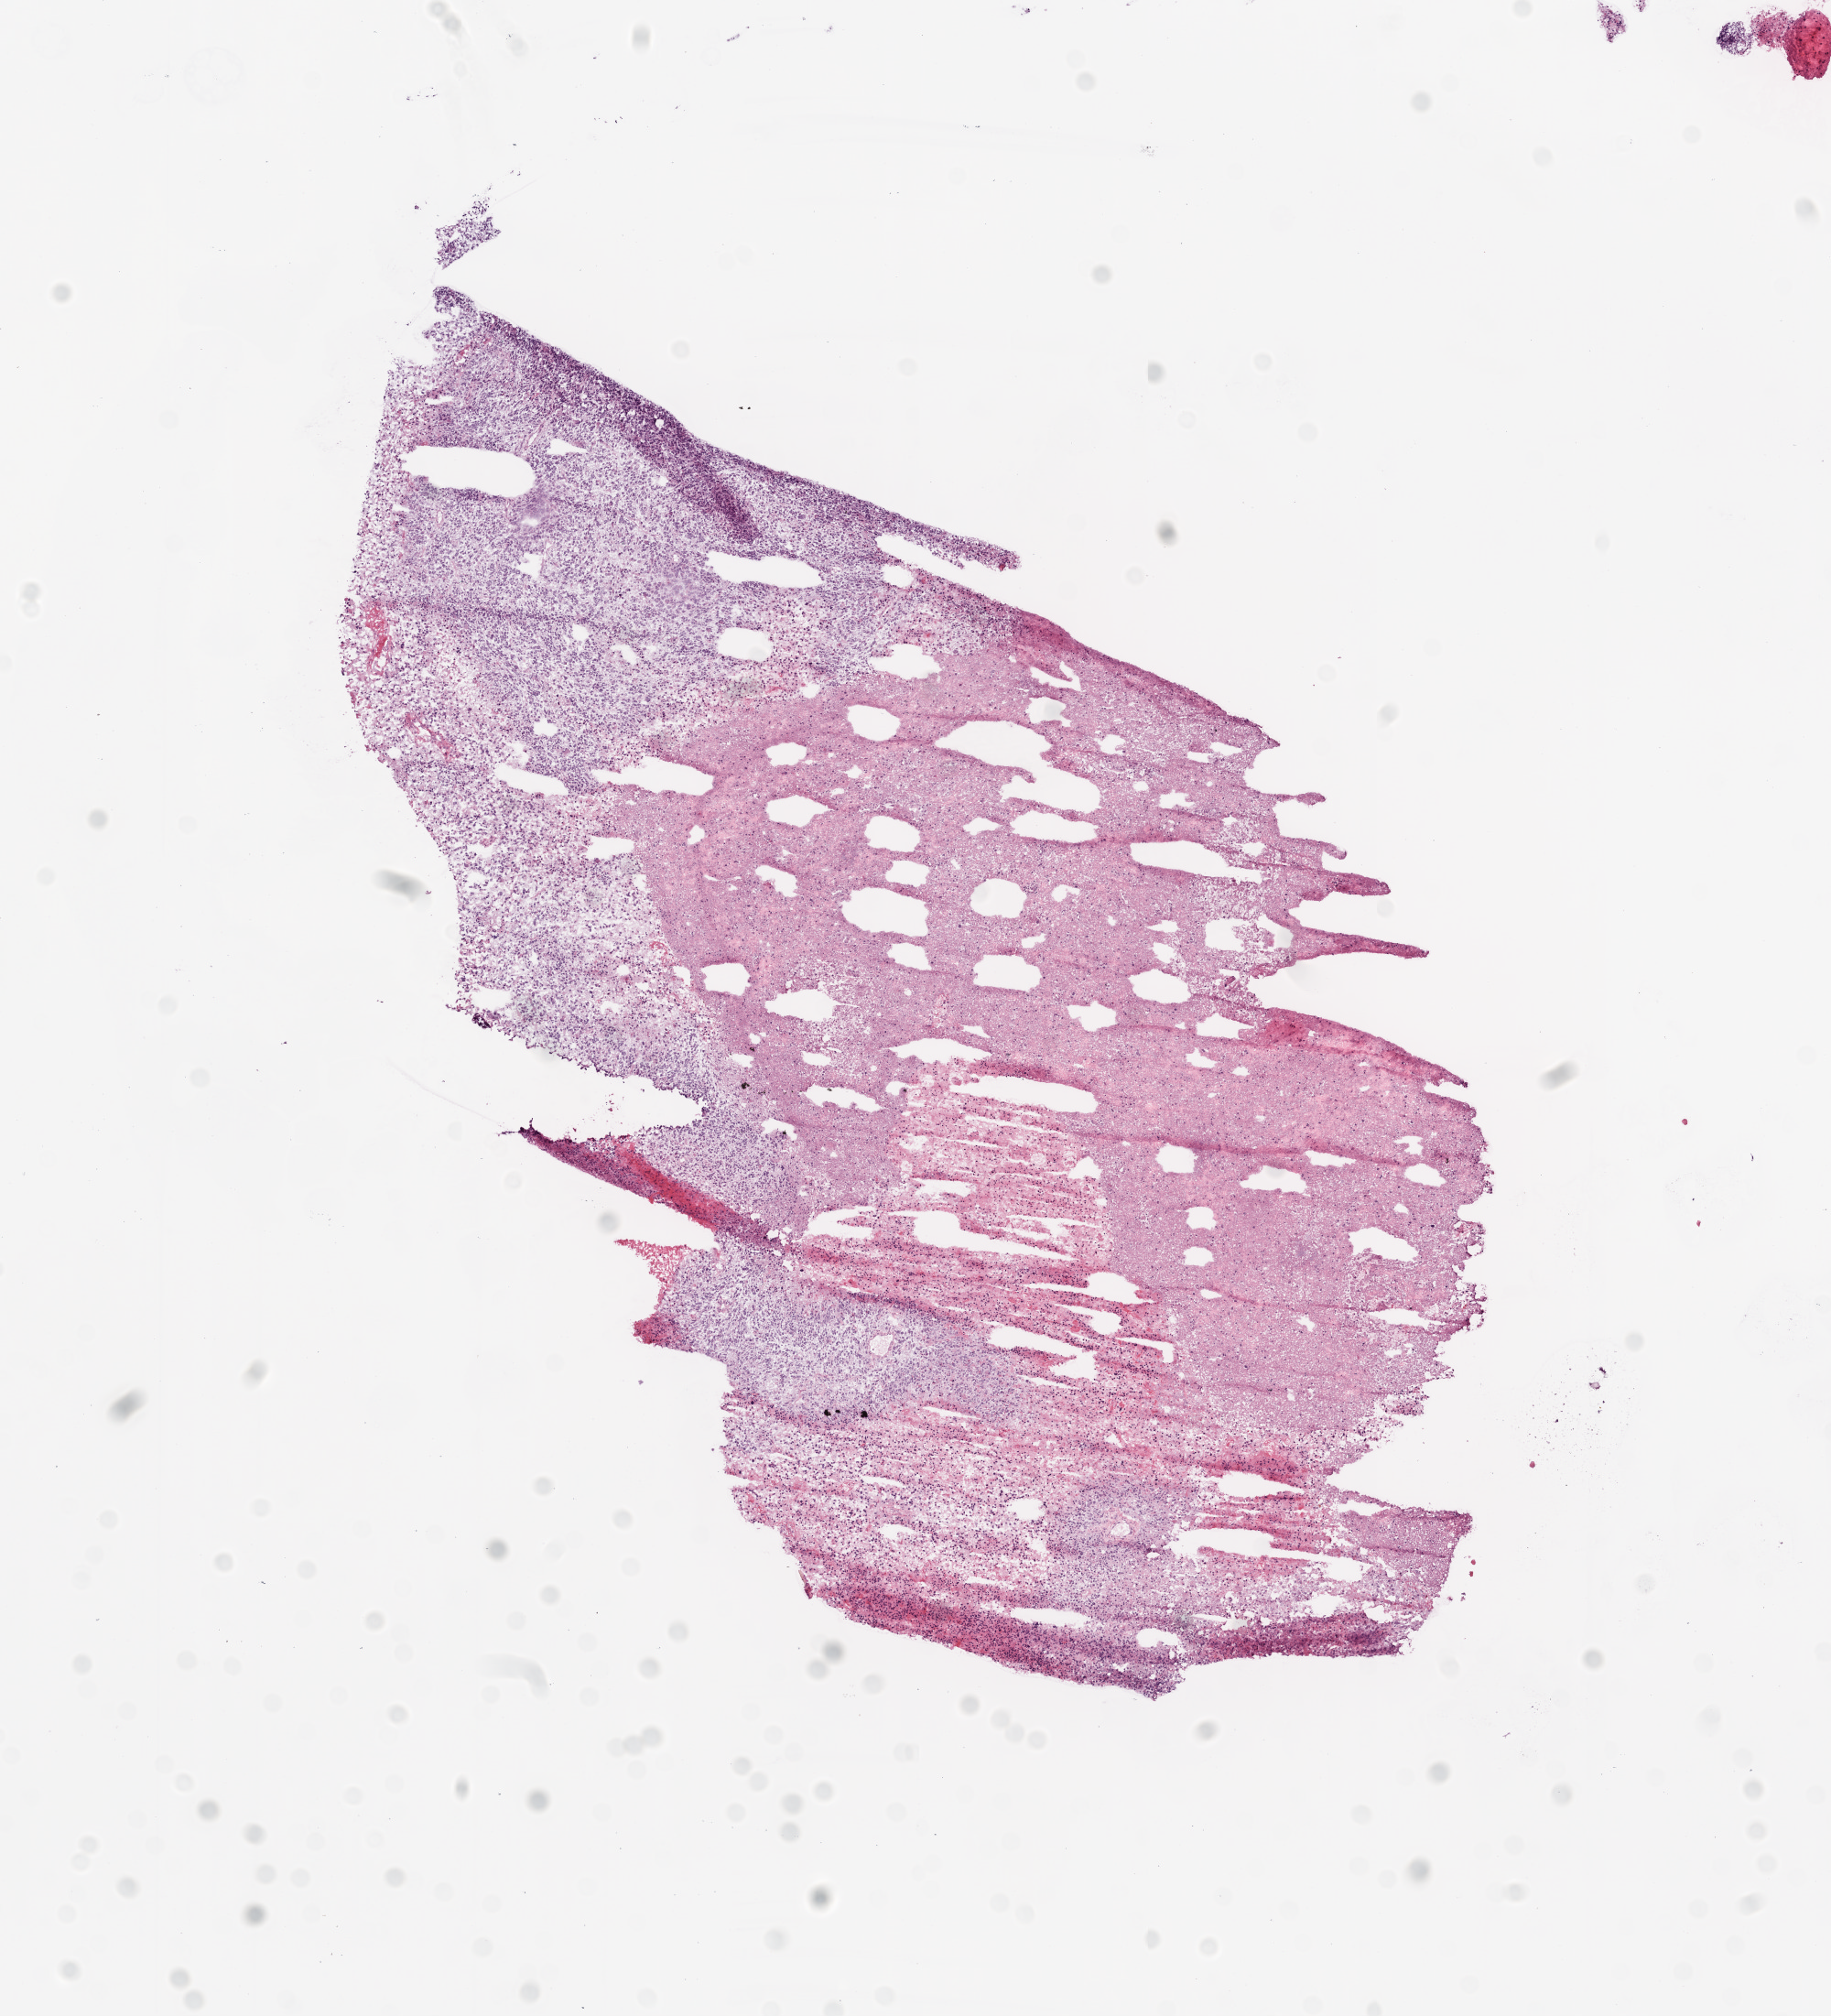
H&E-stained whole-slide image — whole scanned area (about 8.0 x 8.8 mm, slide scanned at 20x) shown as a low-resolution overview, frozen section, sample: primary tumour, brain. Patient: male, age at initial diagnosis 21 years.
Diagnosis: Glioblastoma.